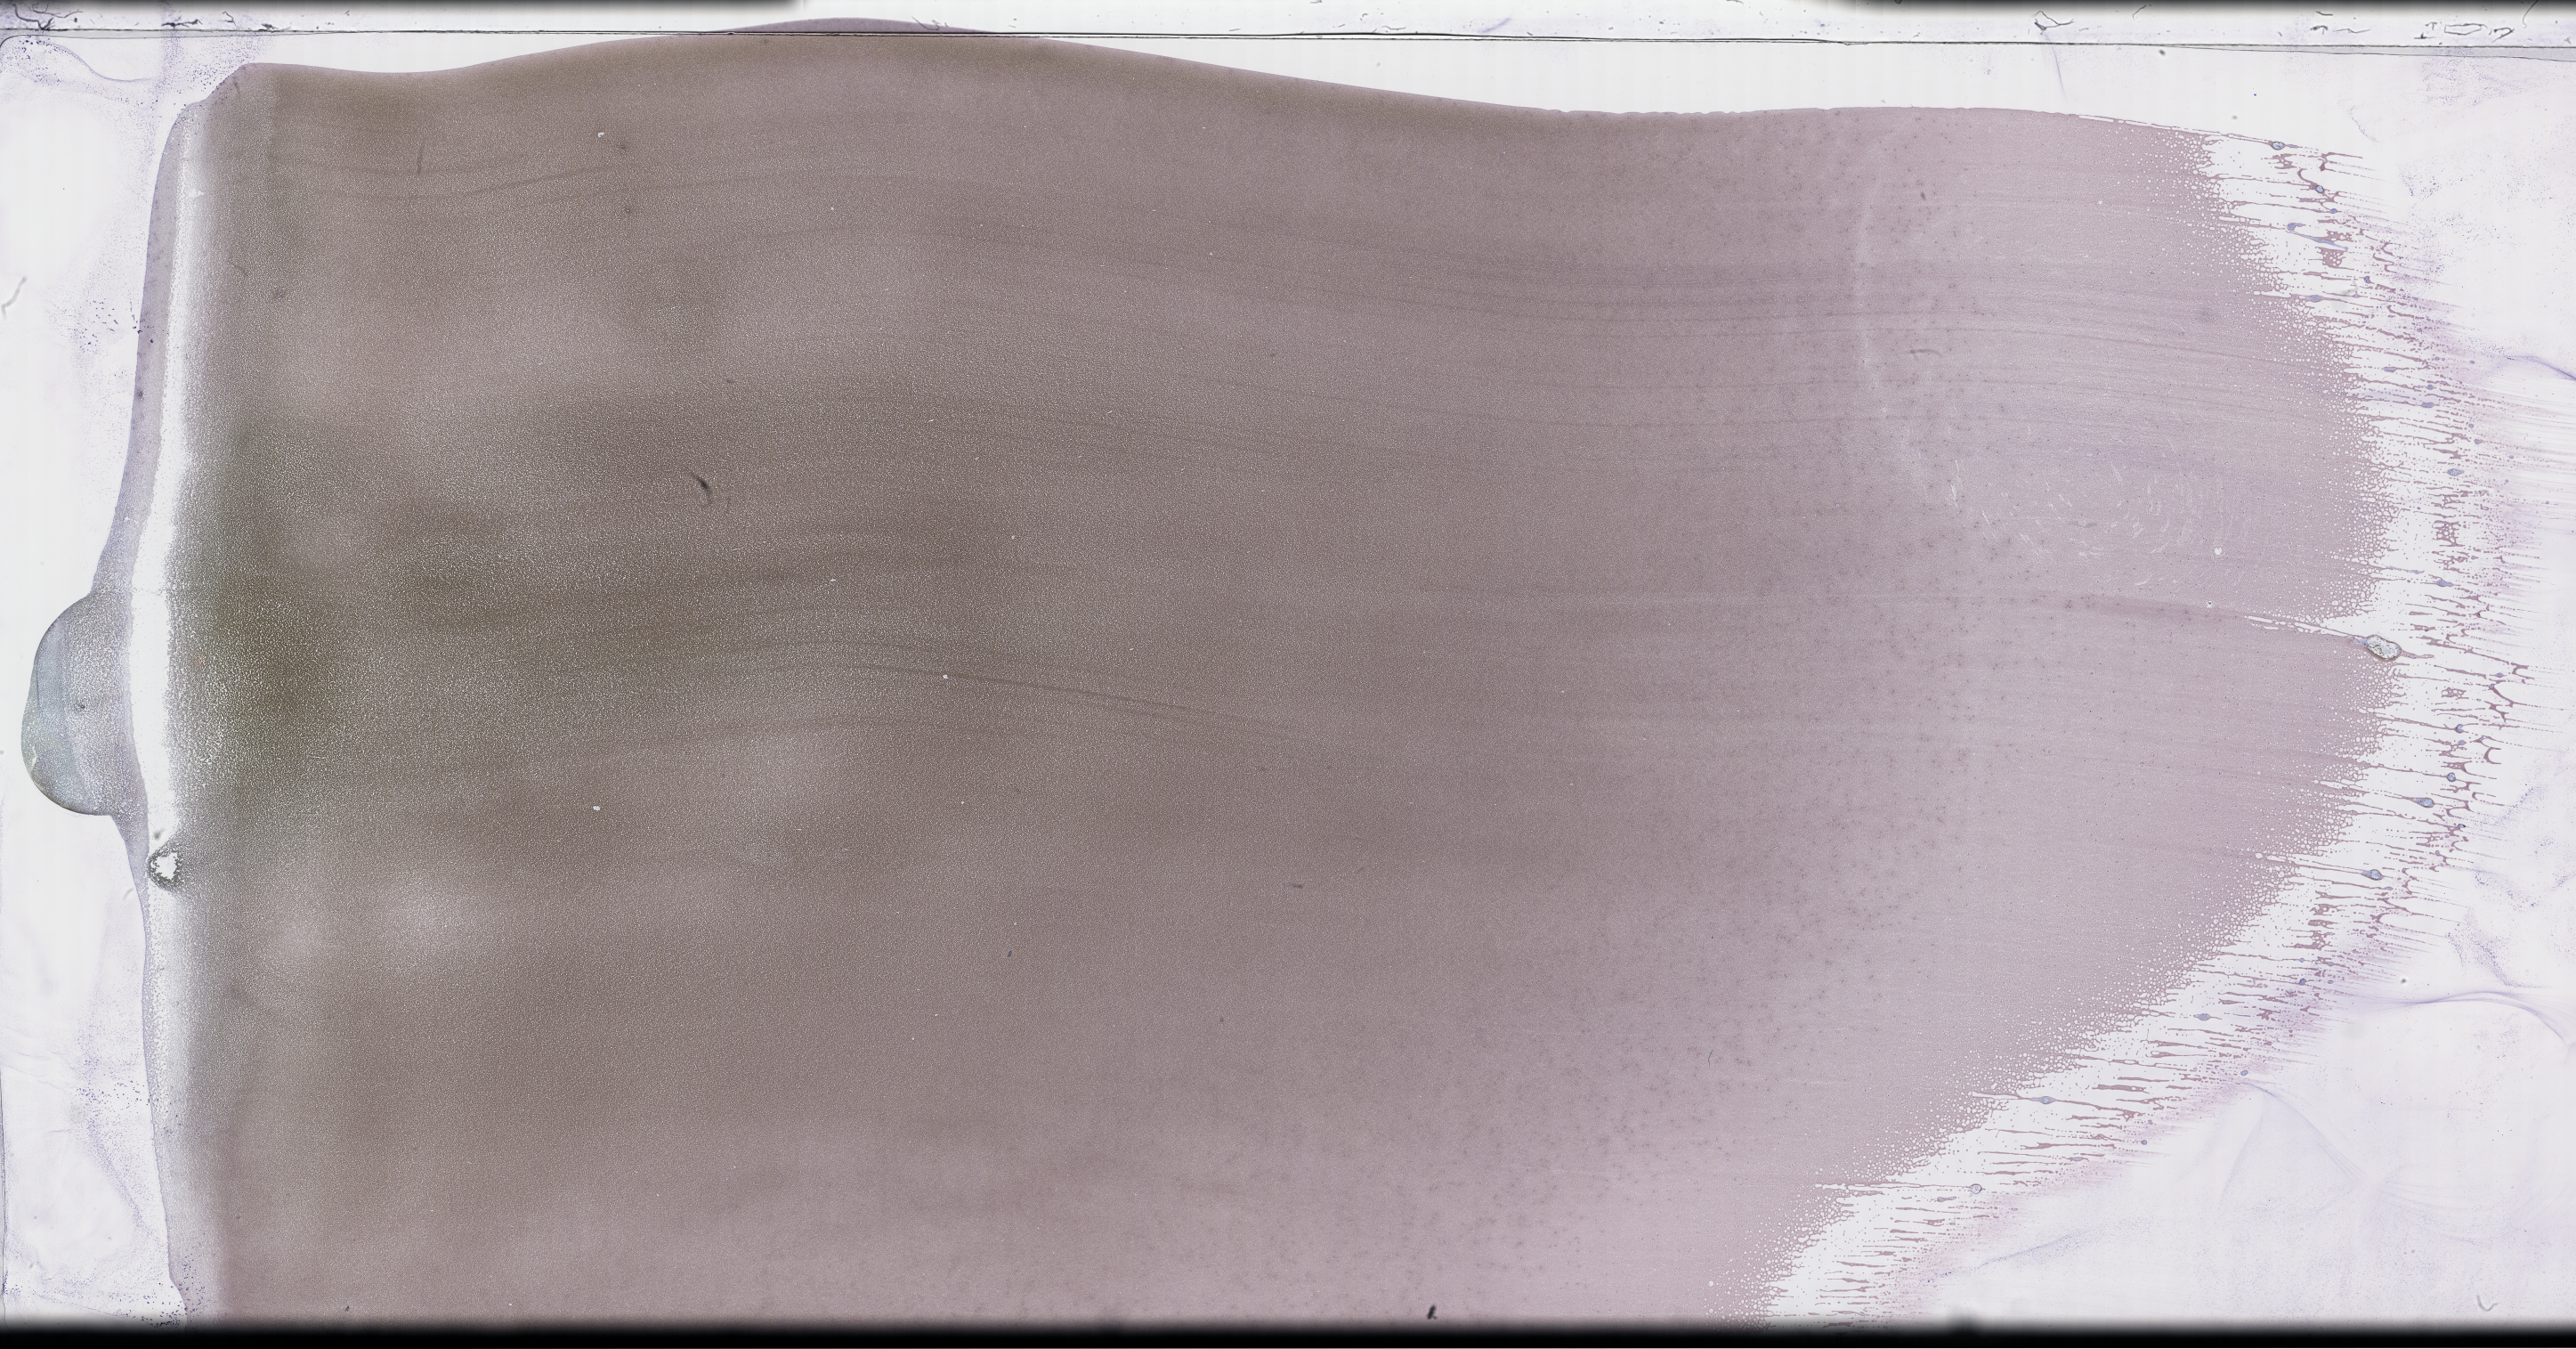
Wright-Giemsa-stained whole blood smear, whole-slide image, a low-resolution overview of the entire scanned area, about 46.7 x 24.5 mm. Patient: male.
From a patient with: Plasma Cell Myeloma.